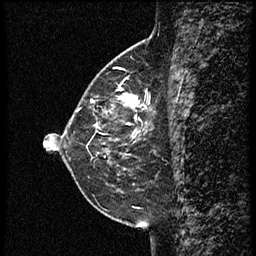
Breast MRI (dynamic contrast-enhanced), one sagittal slice. Position 22 of 60 along the scan axis. Dynamic contrast-enhanced study with each time point stored as its own series, time point 2 of 3 at this slice position (early post-contrast, ordered by acquisition time). 1.5 T. TE 4.2 ms, TR 18.9 ms. 2 mm slice thickness. 256 × 256 image matrix, field of view 200 × 200 mm. Female patient. From the clinical record (not read from this slice): setting: breast cancer imaged before/during neoadjuvant chemotherapy; receptor status: HER2-positive.
Structures marked on this image (semi-automatically segmented with operator editing):
- analysis volume of interest (the breast-tissue region the enhancement analysis was run in; not a lesion): bounding box (x1, y1, x2, y2) in pixels: (77, 80, 161, 147)
- tumour enhancement mask (voxels above the 100 % enhancement threshold inside the analysis volume of interest): (111, 91, 153, 138)